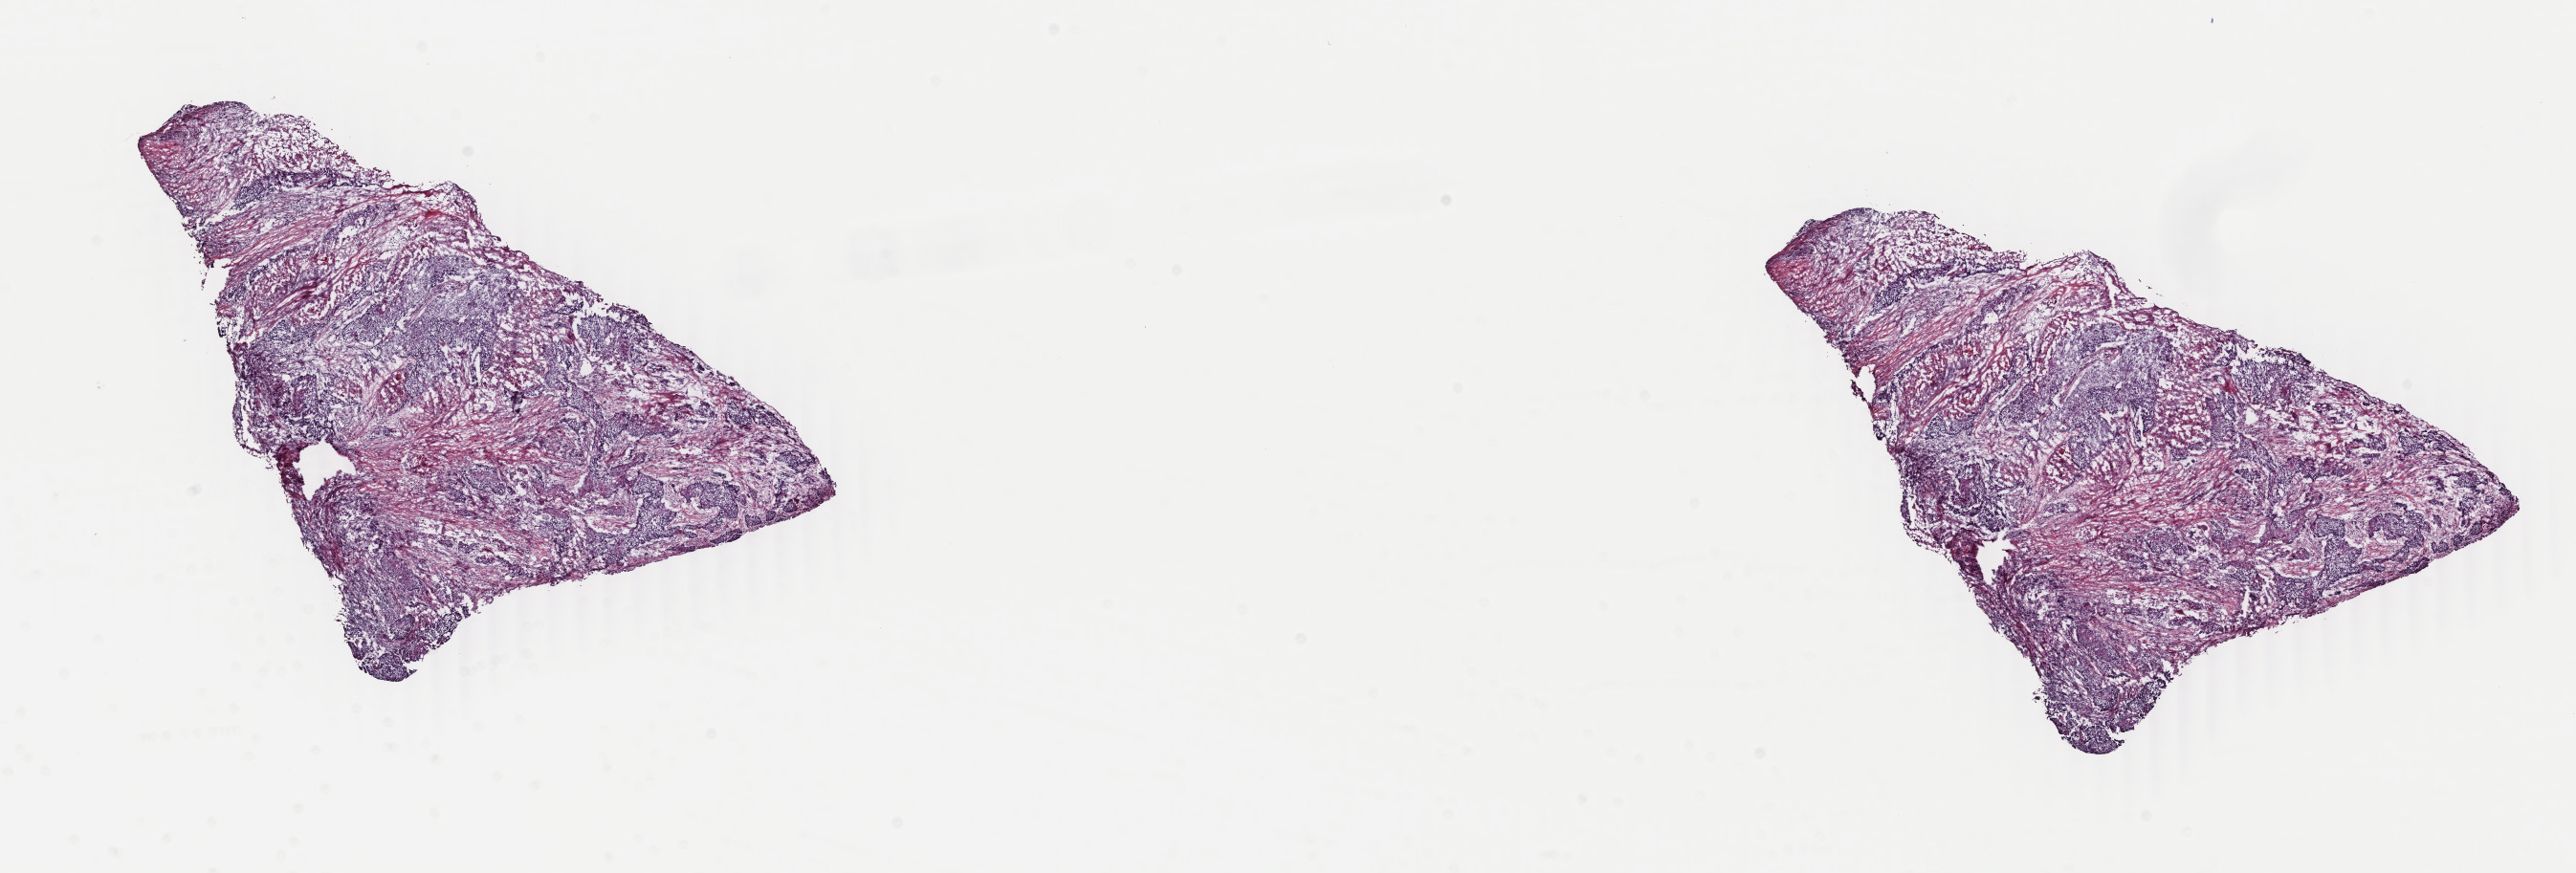
H&E-stained whole-slide image, whole scanned area (about 21.4 x 7.3 mm, from a 40x scan) shown as a low-resolution overview. Frozen section. Sample: primary tumour, lung. Male, age 70 years at initial diagnosis. Composition of this section per pathologist review: tumour cells 50%, tumour nuclei 60%, normal cells 0%, stromal cells 40%, necrosis 10%. Infiltration values recorded for this section: lymphocyte infiltration 0%, monocyte infiltration 0%, neutrophil infiltration 0%.
AJCC pathologic stage: IIB (6th edition). Histologic diagnosis: Squamous cell carcinoma, NOS. Laterality: right.